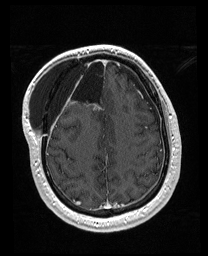
Brain MRI from a brain-tumour surgery series, one axial slice; T1-weighted post-contrast; 1 mm slice thickness; 208 × 256 image matrix. From the clinical record (not read from this slice): histopathology: Astrocytoma; WHO grade: 4; IDH mutation: yes.
Annotated regions visible in this slice (manually delineated by an expert):
- previous resection cavity: box from (x=56, y=57) to (x=106, y=101) px